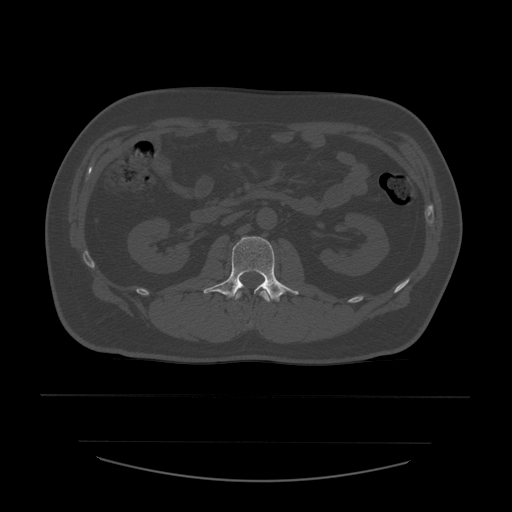
CT including the spine, one axial slice. Slice 205 of 532 in the series (ordered by position). Reconstruction kernel STANDARD. 120 kVp. Bone window (W 1800 / L 400 HU). 1.25 mm slice thickness. 512 × 512 image matrix, field of view 441 × 441 mm. Patient age 44 years. From the clinical record (not read from this slice): primary cancer: soft tissue sarcoma.
Outlined on this slice (semi-automatically segmented with operator editing):
- L1 vertebra: box from (x=235, y=290) to (x=272, y=324) px
- L2 vertebra: (x=204, y=237)–(x=299, y=302)